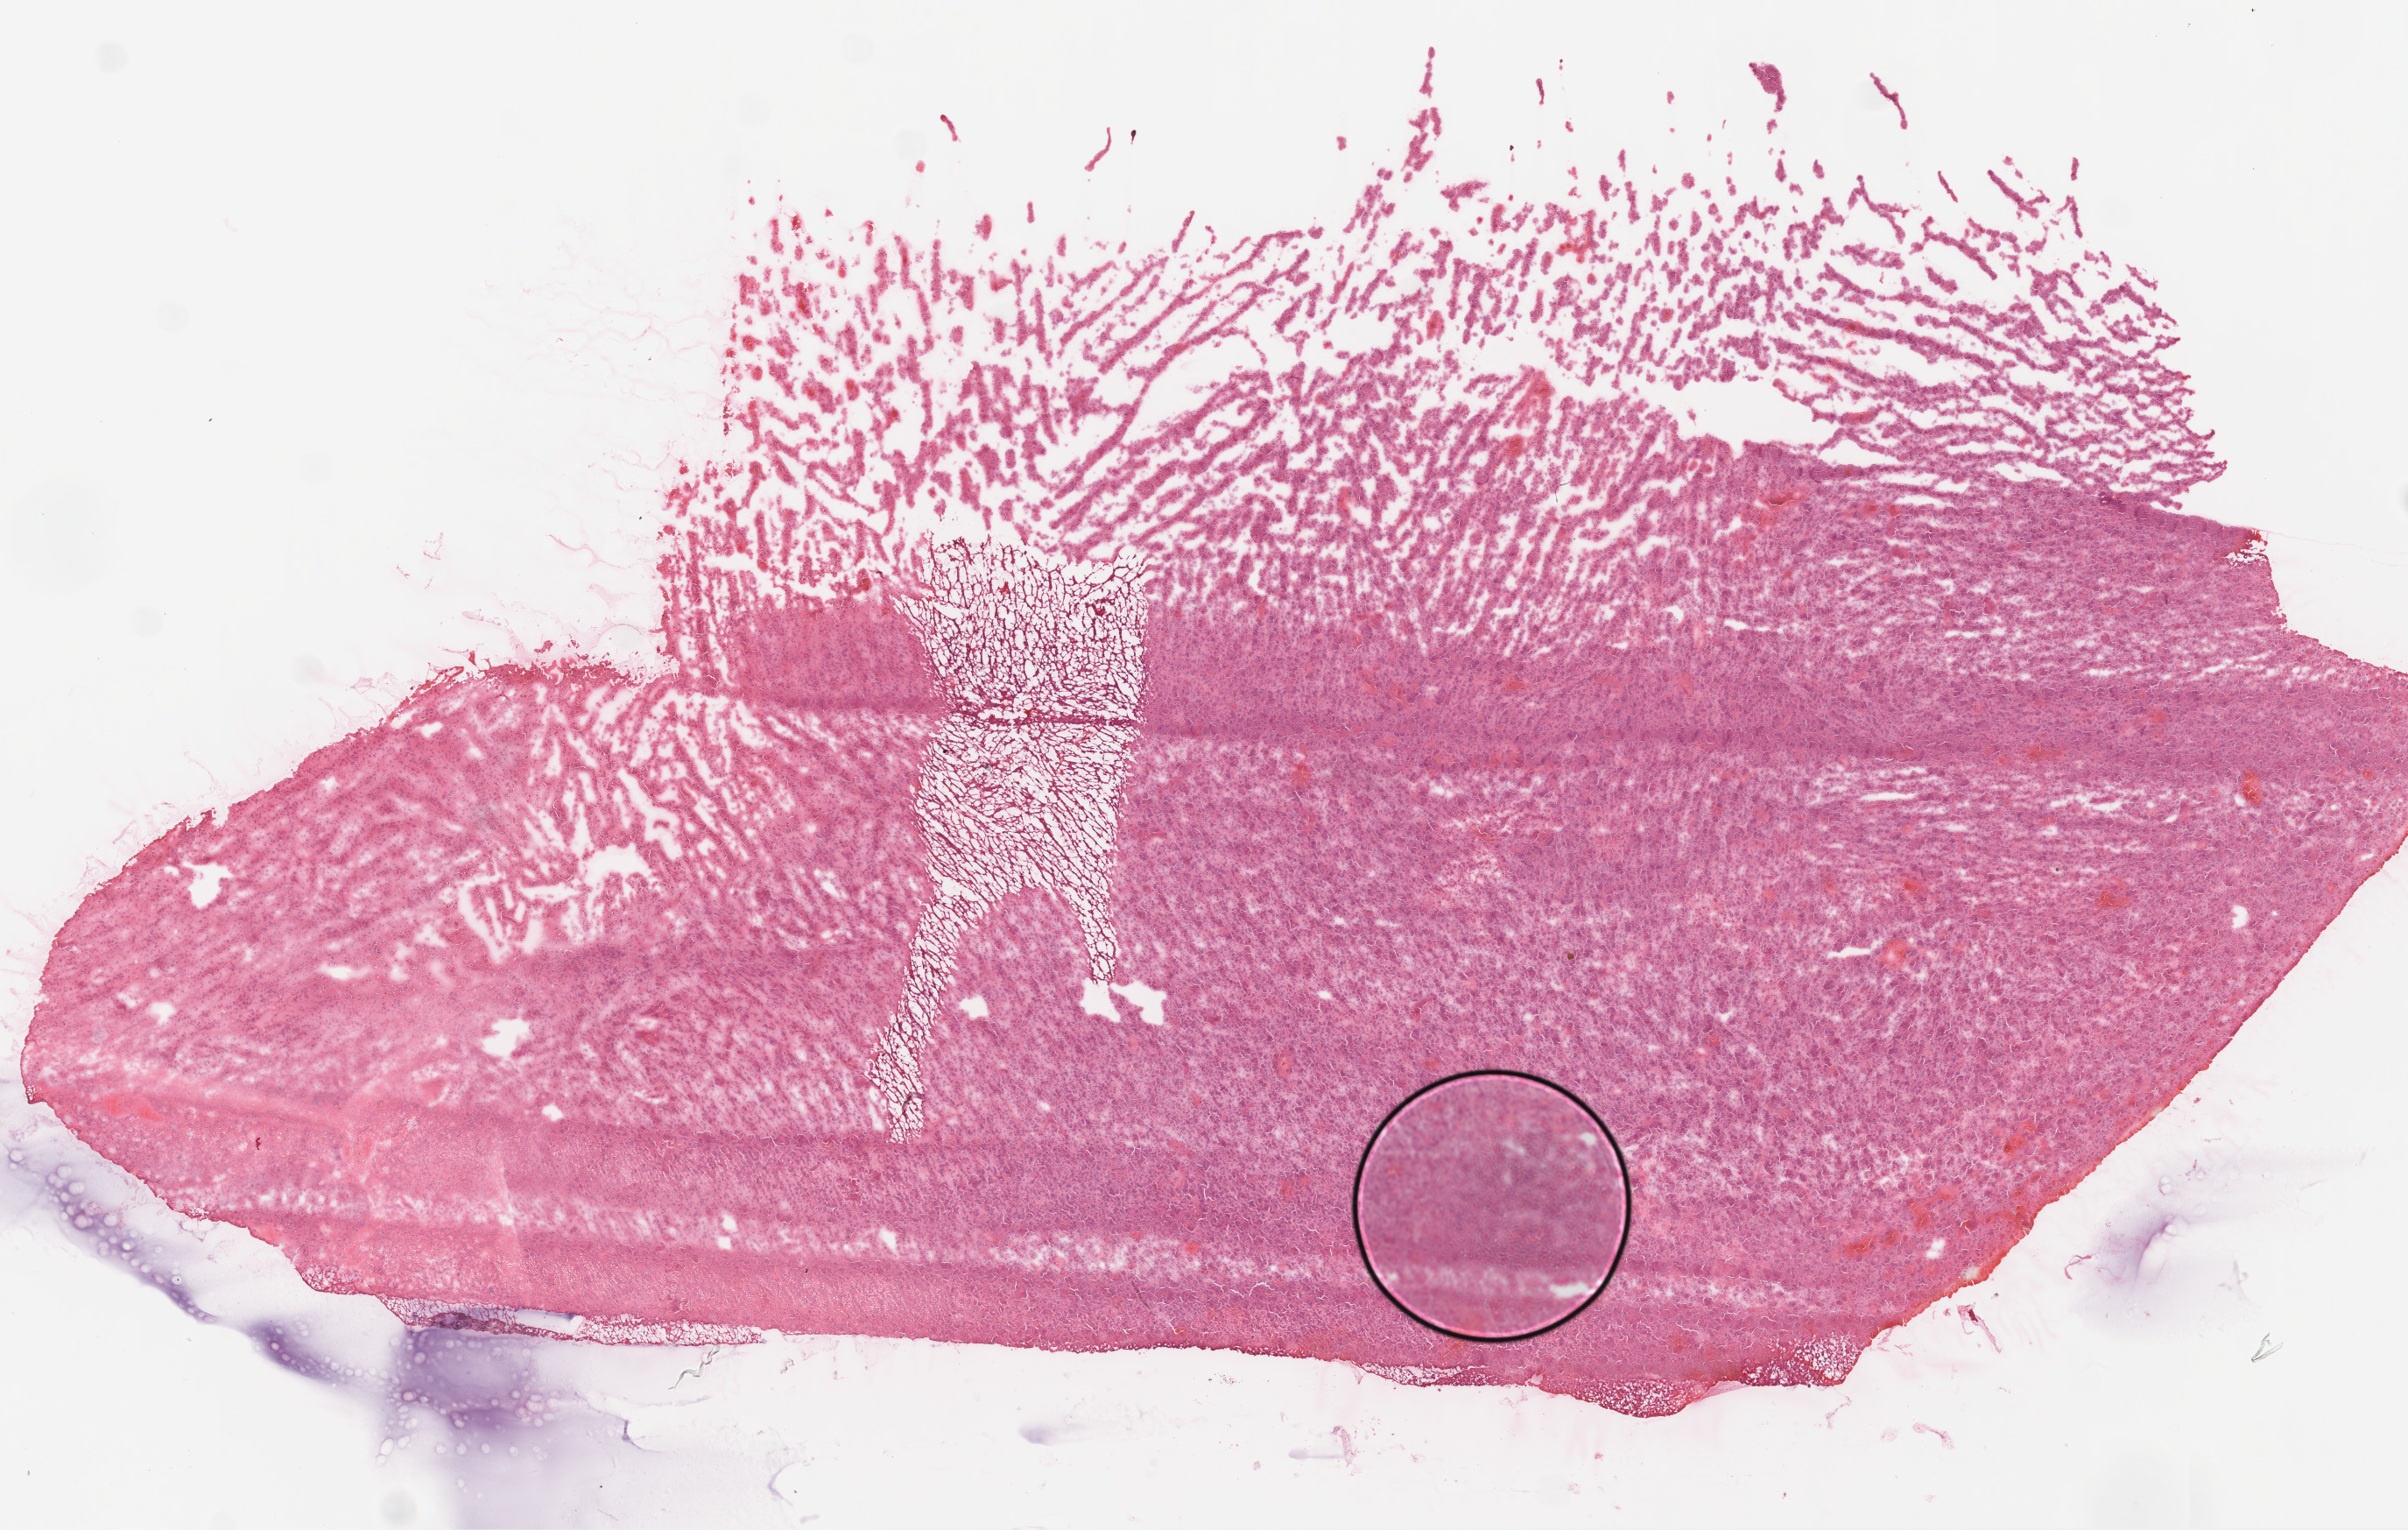
Whole-slide histology image, Hematoxylin and eosin (H&E) stained — low-resolution overview of the scanned area, about 11.0 x 7.0 mm; frozen section from the top of the tissue portion; sample: primary tumour, brain. Patient: female, age at initial diagnosis 61 years. Composition of this section per pathologist review: tumour cells 50%, tumour nuclei 85%, normal cells 0%, stromal cells 10%, necrosis 40%.
* histologic diagnosis: Glioblastoma